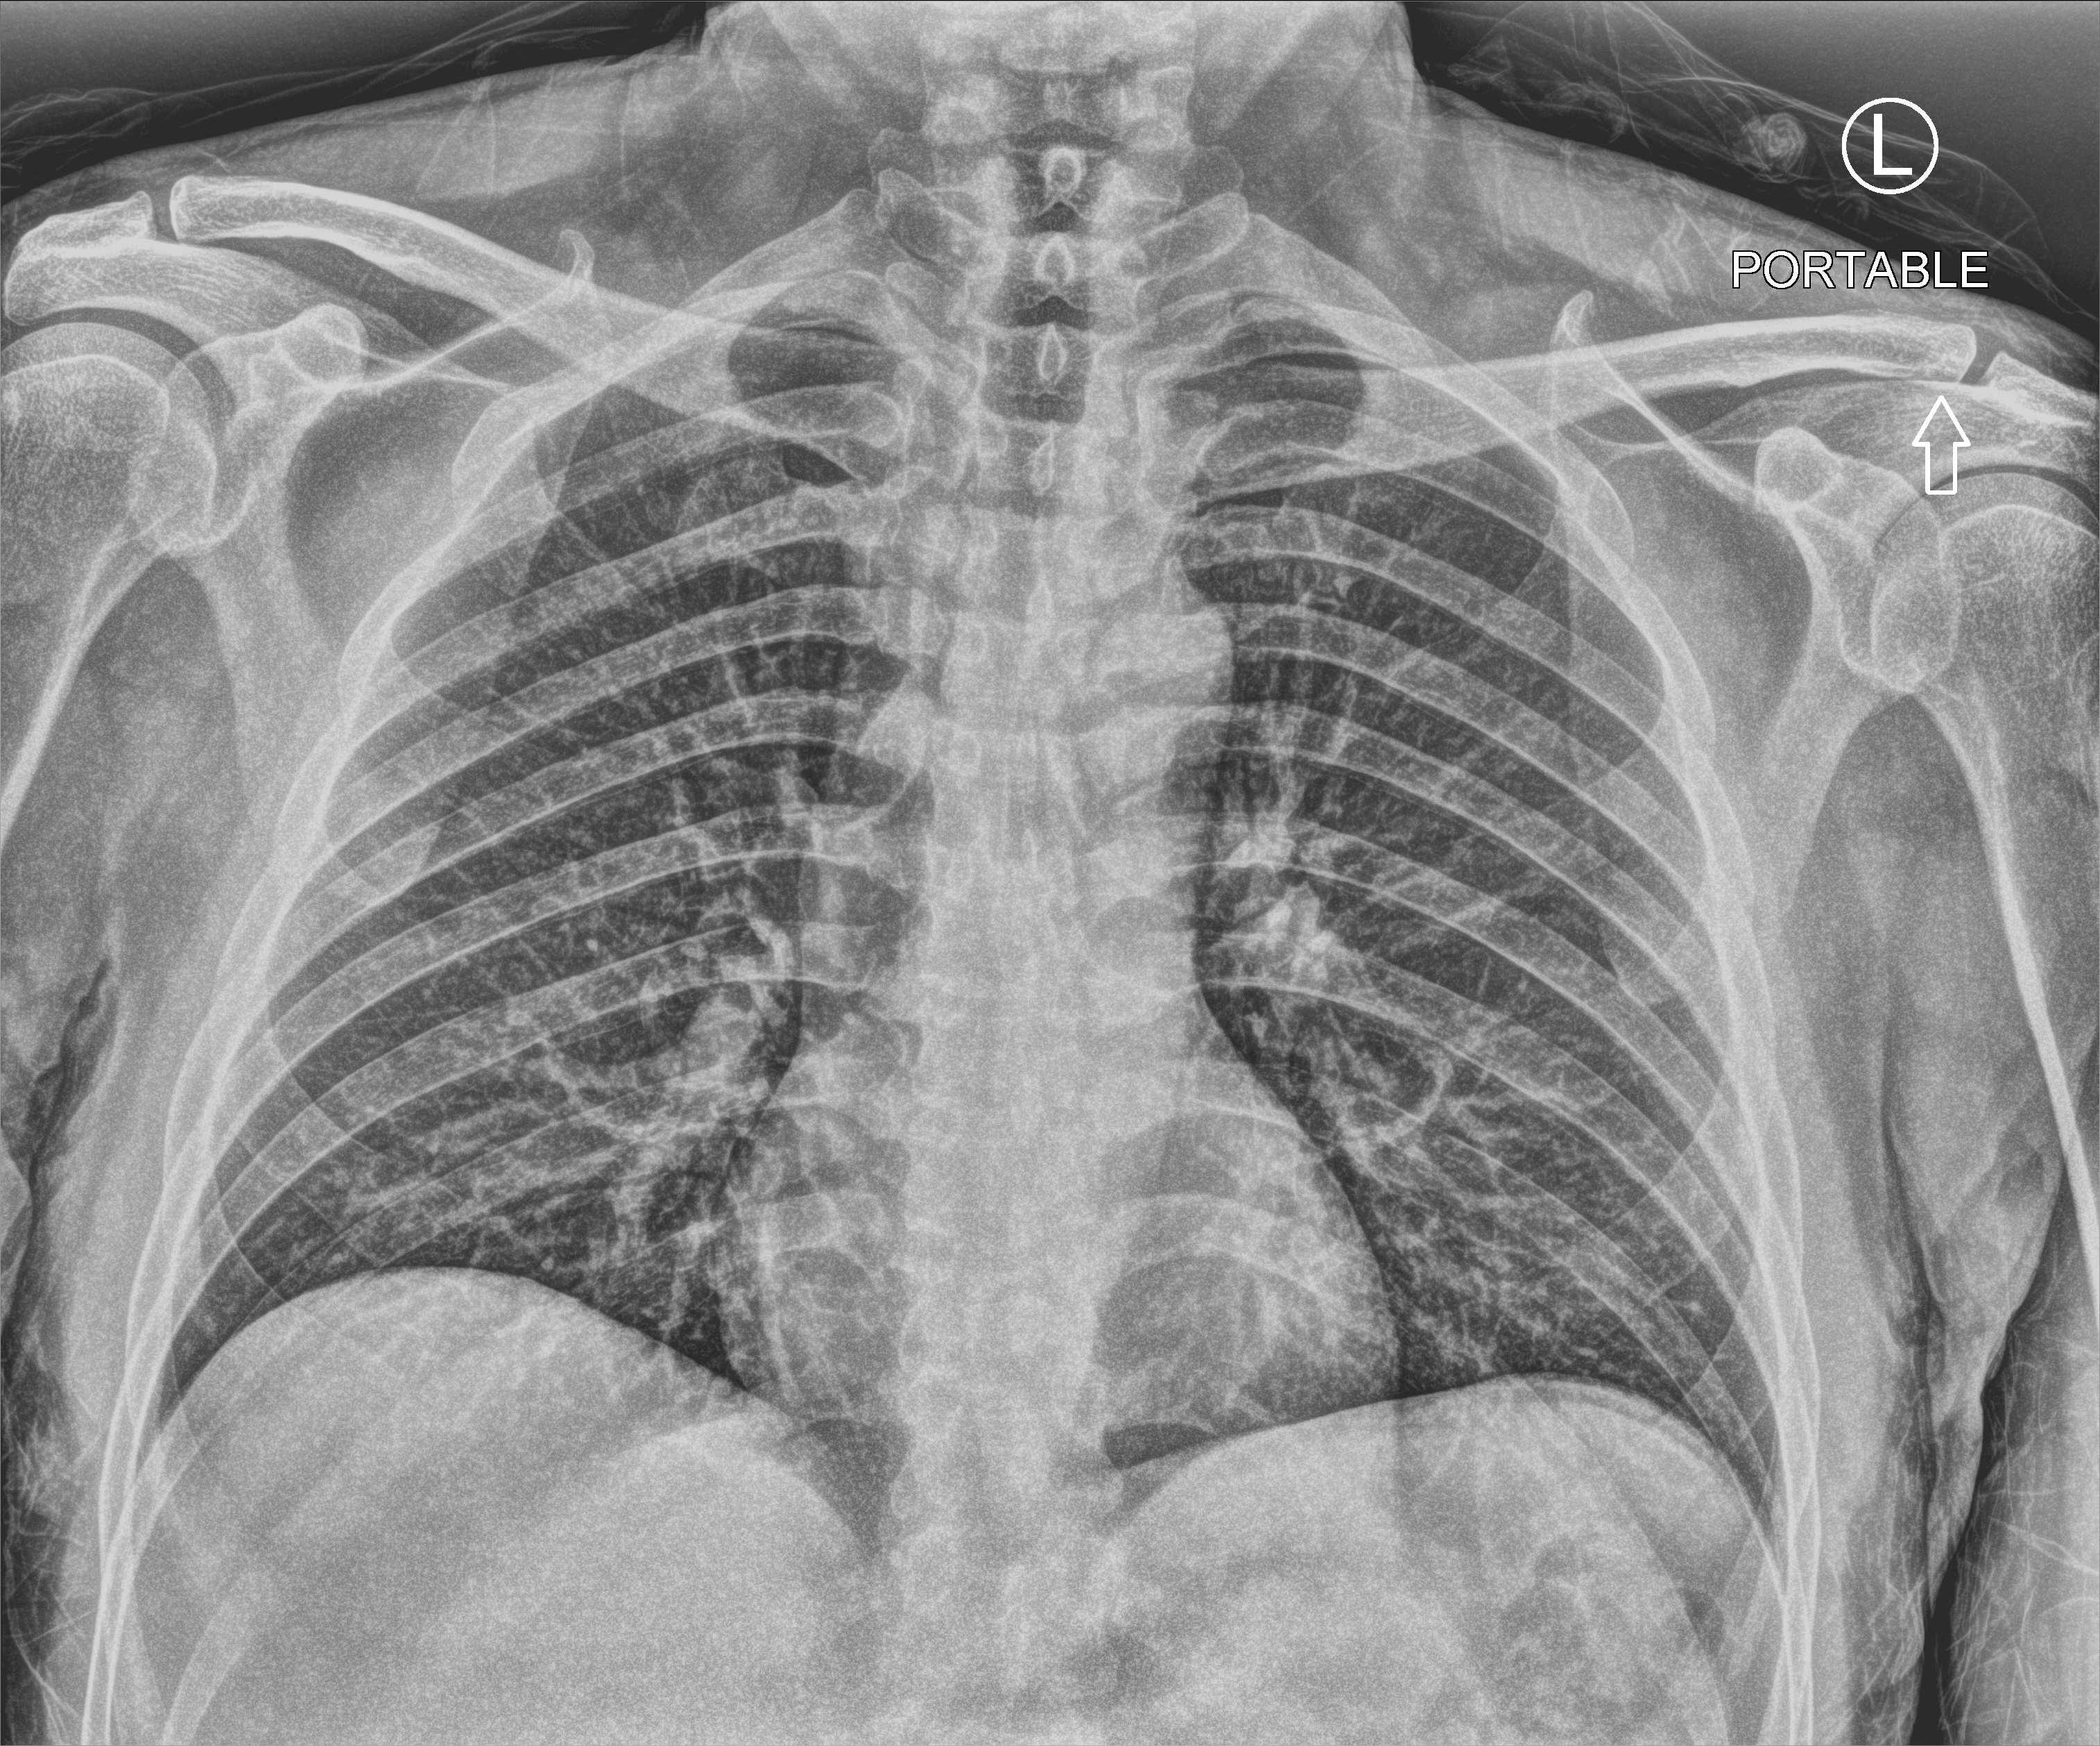
Chest X-ray (portable); anteroposterior (AP) projection. Male patient hospitalised with COVID-19, age 18–59 years.
From the hospital-stay record, not from the radiograph (when in the stay this image was taken is not recorded): mechanically ventilated during this hospital stay: no.